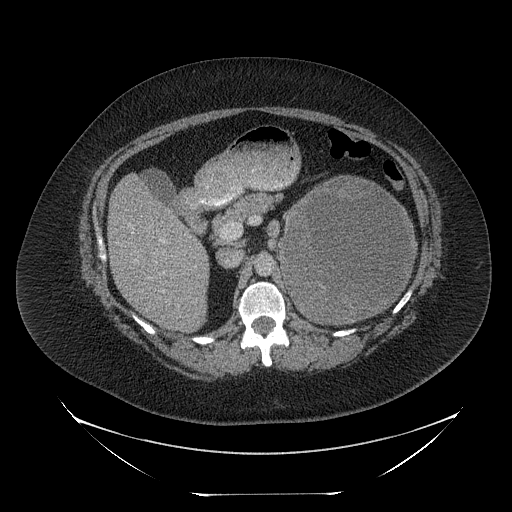
Contrast-enhanced abdominal CT, one axial slice; position 140 of 205 along the scan axis; reconstruction kernel STANDARD; intravenous contrast given; soft-tissue window (W 400 / L 40 HU); 2.5 mm slice thickness; 512 × 512 image matrix. Patient: female, 53 years. From the clinical record (not read from this slice): diagnosis: adrenocortical carcinoma; tumour side: left adrenal; tumour size at pathology: 17 cm; Ki-67 index: 20 %; stage (as recorded): 3.
Outlined on this slice (semi-automatic segmentation, software-assisted and operator-edited):
- mass: bounding box [x1, y1, x2, y2] px = [282, 179, 412, 320]